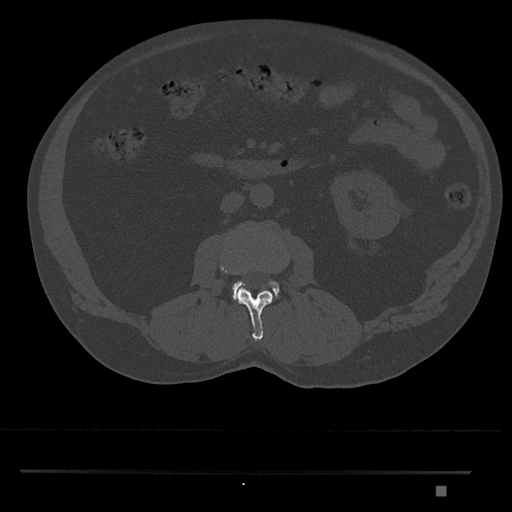
CT including the spine, one axial slice. Slice 724 of 1134 in the series (ordered by position). Reconstruction kernel Br40s/3. 120 kVp. Bone window (W 1800 / L 400 HU). 0.5 mm slice thickness. 512 × 512 image matrix, field of view 429 × 429 mm. Male patient, age 65 years. Case-level facts recorded for this patient, not image findings: primary cancer: prostate.
Structures marked on this image (semi-automatically segmented with operator editing):
- L2 vertebra: box from (x=220, y=264) to (x=273, y=341) px
- L3 vertebra: (x=232, y=280)–(x=279, y=300)